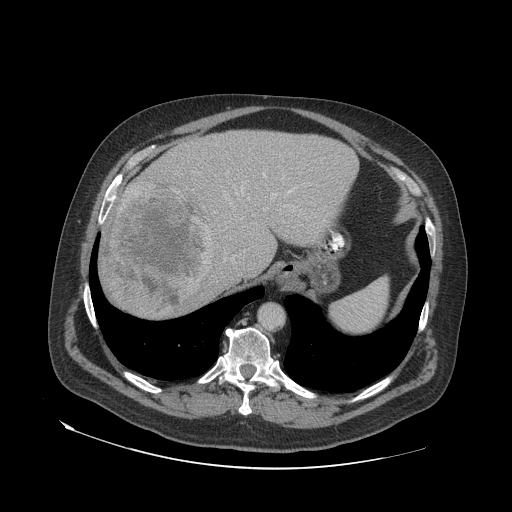
Contrast-enhanced abdominal CT (liver protocol), one axial slice. Slice 56 of 79 in the series (ordered by position). 140 kVp. Soft-tissue window (W 400 / L 40 HU). 2.5 mm slice thickness. 512 × 512 image matrix, field of view 480 × 480 mm. Case-level facts recorded for this patient, not image findings: diagnosis: hepatocellular carcinoma (patient treated with transarterial chemoembolisation; whether this scan precedes or follows treatment is not stated here); TNM stage (as recorded): Stage-IVA; Child-Pugh class: A.
Structures marked on this image (semi-automatically segmented with operator editing):
- abdominal aorta: bounding box (x1, y1, x2, y2) in pixels: (260, 304, 283, 328)
- liver parenchyma outside the tumour (the mass and vessels are separate outlines, so this box may not span the whole liver): (100, 130, 358, 316)
- mass: (103, 180, 215, 314)
- liver vessels: (242, 173, 292, 196)